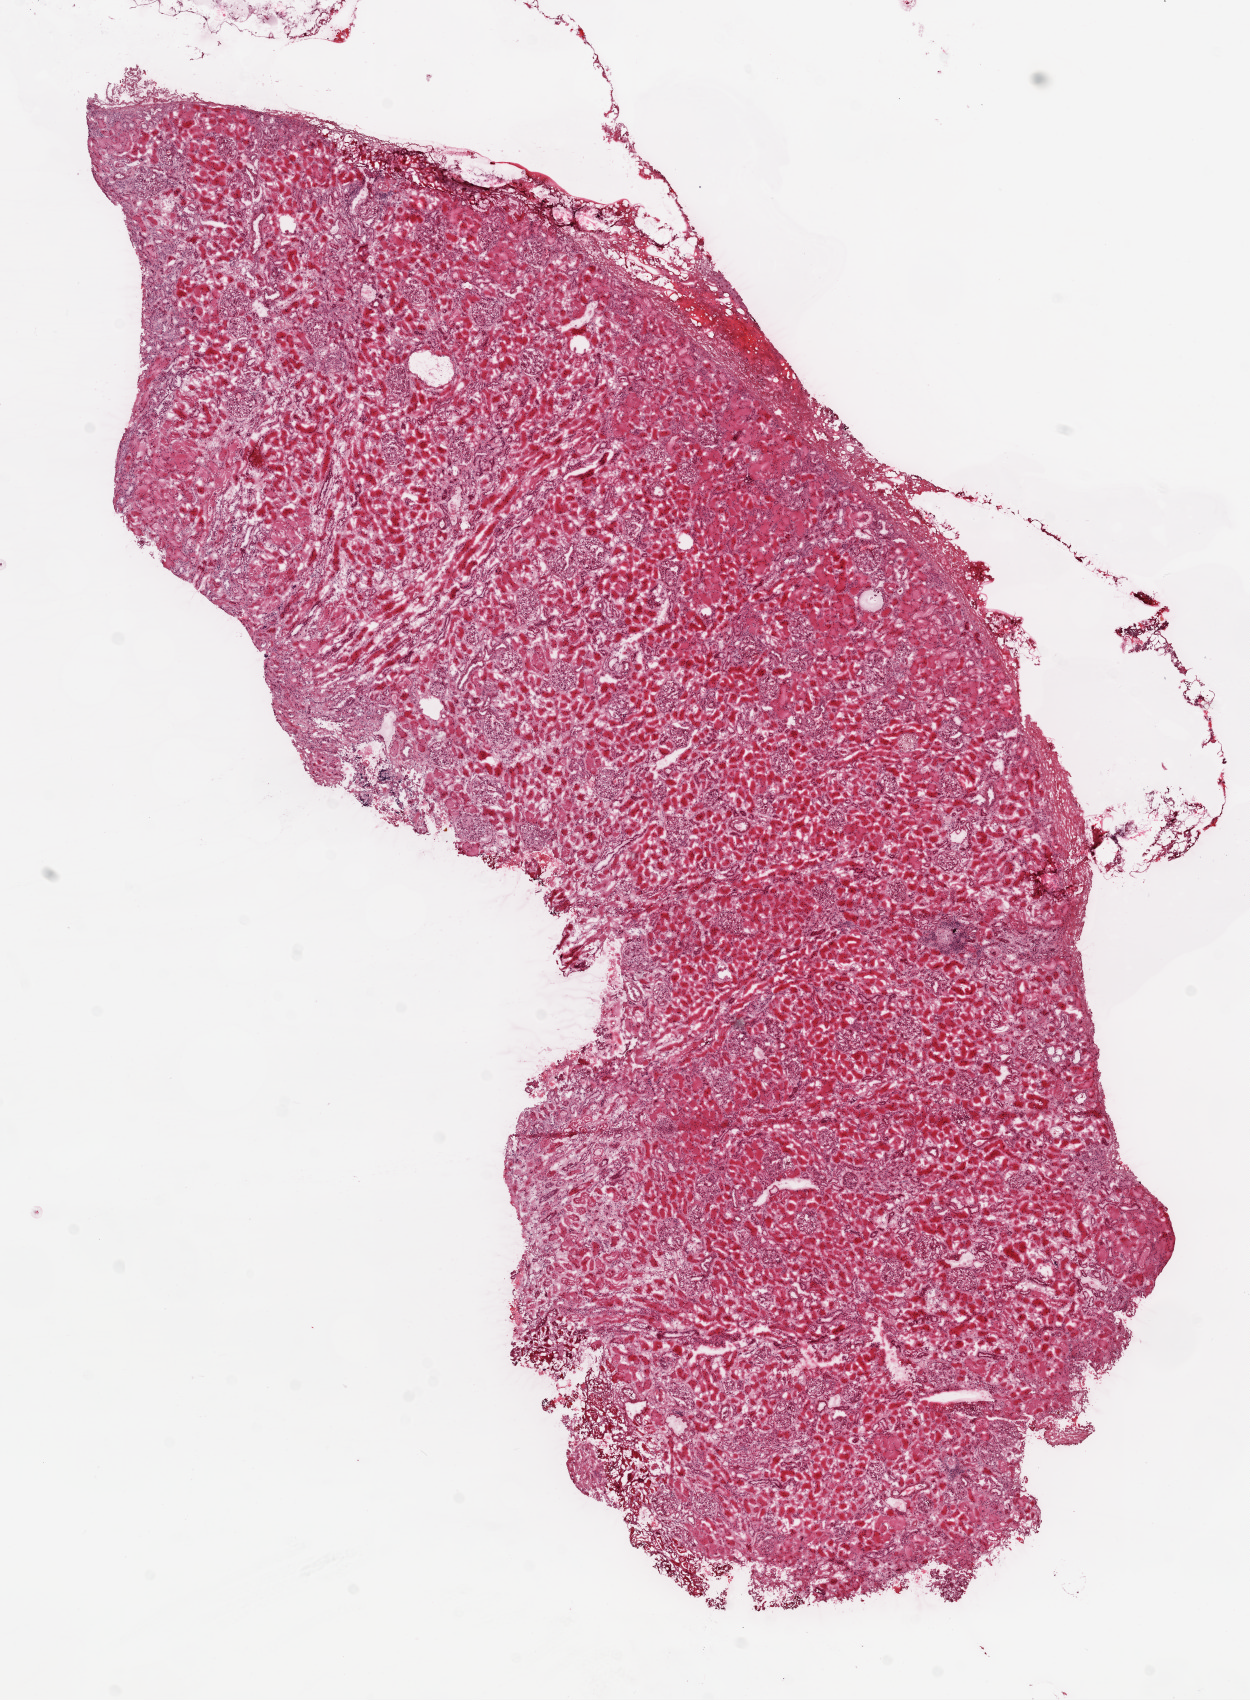
Whole-slide histology image, Hematoxylin and eosin (H&E) stained, low-resolution overview of the scanned area, about 10.0 x 13.6 mm. Frozen section from the top of the tissue portion. Solid tissue normal (non-tumour tissue) sample from the kidney. Male, age 54 years at initial diagnosis.
This section: solid tissue normal (non-tumour) sample from the same patient. Patient diagnosis: Clear cell adenocarcinoma, NOS.